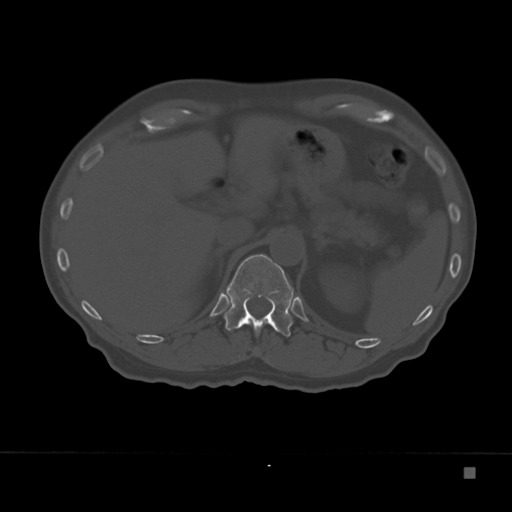
CT including the spine, one axial slice. Reconstruction kernel Br40s. Bone window (W 1800 / L 400 HU). 512 × 512 image matrix. Patient: male, 72 years. Case-level facts recorded for this patient, not image findings: primary cancer: skeletal.
Structures marked on this image (semi-automatic segmentation, software-assisted and operator-edited):
- T12 vertebra: bounding box [x1, y1, x2, y2] px = [225, 254, 294, 337]